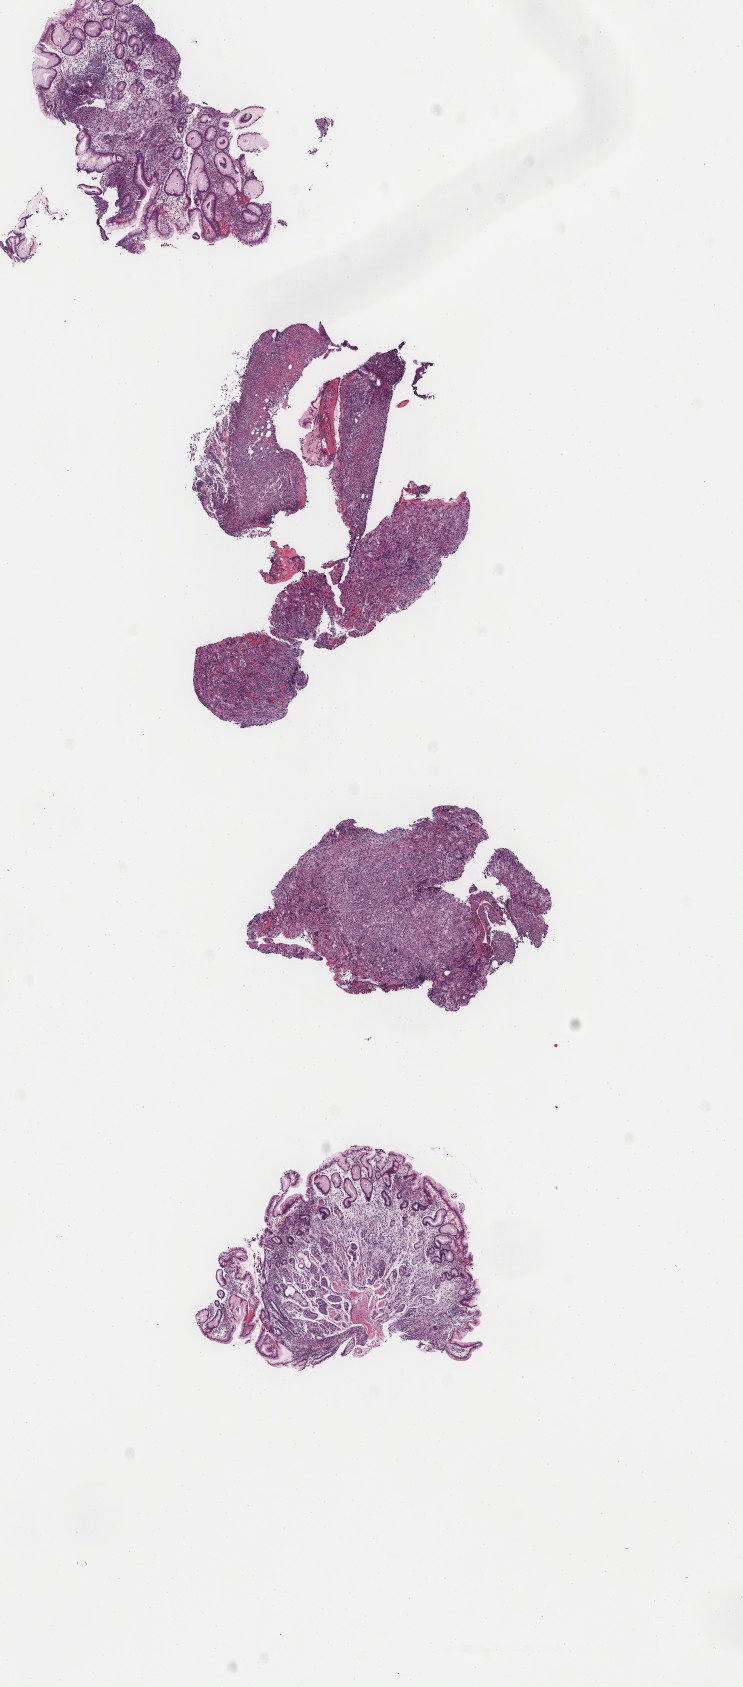
Digitized H&E-stained tissue section (whole slide), shown as a low-resolution overview of the whole scanned area (about 5.9 x 13.4 mm), formalin-fixed paraffin-embedded (FFPE) diagnostic section, sample: primary tumour, stomach. Patient: male, age at initial diagnosis 78 years. Histologic grade: G3 (poorly differentiated).
AJCC pathologic stage: IIIA (6th edition). Diagnosis: Carcinoma, diffuse type. TNM: T3 N1 M0.